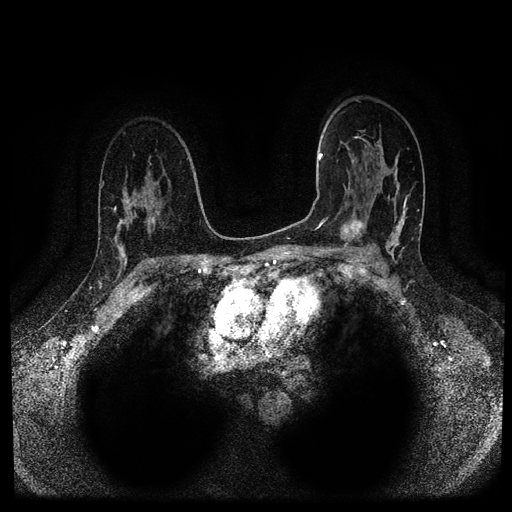
Breast MRI (dynamic contrast-enhanced, multi-phase), one axial slice; position 67 of 116 along the scan axis; dynamic contrast-enhanced series, time point 2 of 5 at this slice position (early post-contrast); 1.5 T; TE 2.6 ms, TR 5.3 ms; 2 mm slice thickness; 512 × 512 image matrix. Patient: female, 44 years.
Structures marked on this image (semi-automatic segmentation, software-assisted and operator-edited):
- breast lesion (labelled 'tumour' in the annotation; benign lesions carry a separate 'benign' label): bounding box (x1, y1, x2, y2) in pixels: (335, 215, 367, 247)